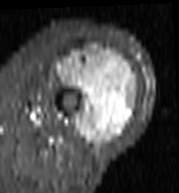
MRI of an extremity soft-tissue mass, one axial slice. Position 49 of 103 along the scan axis. STIR. MR volume resampled by the dataset authors to the PET/CT grid (not the native acquisition matrix). 3.27 mm slice thickness. 179 × 193 image matrix. Female patient. Case-level facts recorded for this patient, not image findings: histological type: undifferentiated – high grade; grade: high; site of the primary tumour: left thigh.
Outlined on this slice (expert contour drawn on MRI and transferred to this co-registered scan by the dataset authors):
- gross tumour volume including surrounding oedema: bounding box <52,44,138,148> (left, top, right, bottom; pixels)
- gross tumour volume (mass): <57,50,138,148>